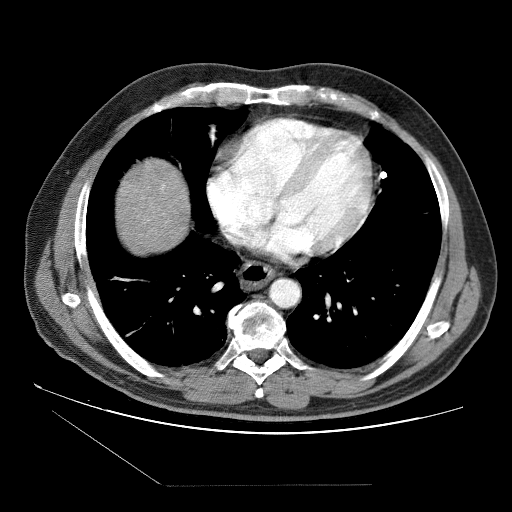
Contrast-enhanced abdominal CT (liver protocol), one axial slice. Position 82 of 87 along the scan axis. 120 kVp. Soft-tissue window (W 400 / L 40 HU). 512 × 512 image matrix, field of view 400 × 400 mm. Case-level facts recorded for this patient, not image findings: diagnosis: hepatocellular carcinoma (patient treated with transarterial chemoembolisation; whether this scan precedes or follows treatment is not stated here); TNM stage (as recorded): Stage-II; Child-Pugh class: B; tumour differentiation: no biopsy; tumour nodularity: multinodular.
Structures marked on this image (semi-automatic segmentation, software-assisted and operator-edited):
- liver parenchyma outside the tumour (the mass and vessels are separate outlines, so this box may not span the whole liver): bounding box (x1, y1, x2, y2) in pixels: (116, 158, 188, 250)